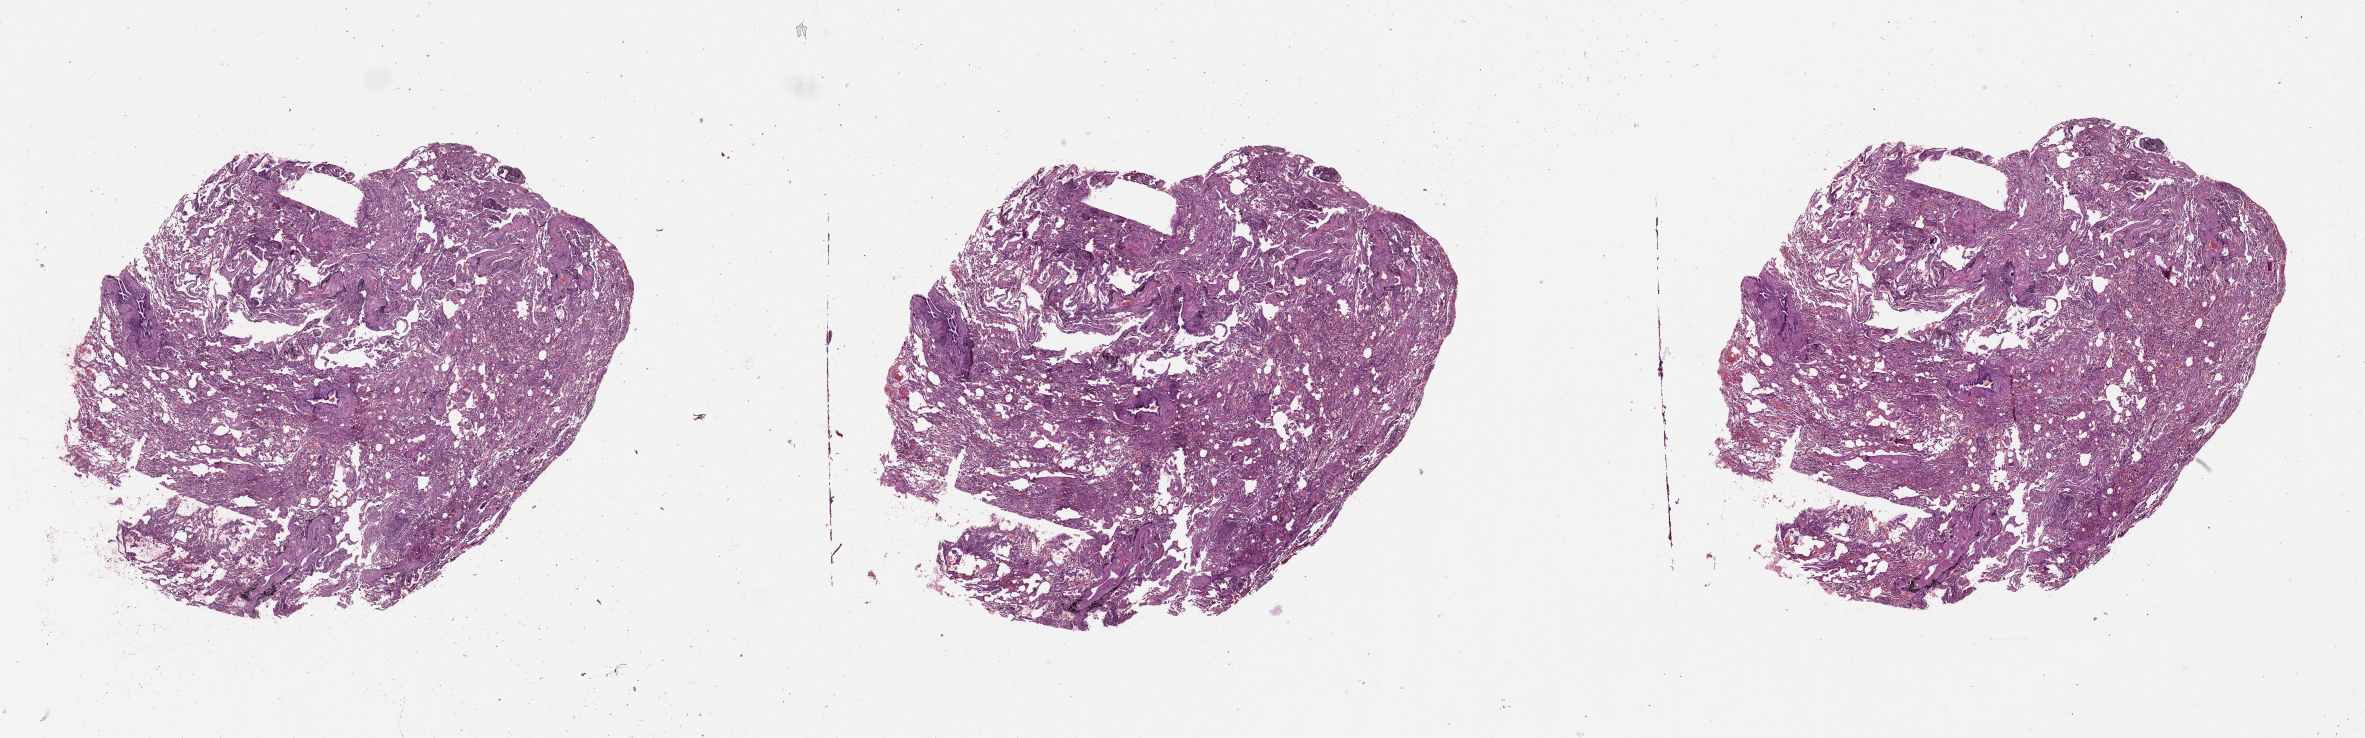
Digitized H&E-stained tissue section (whole slide), a low-resolution overview of the entire scanned area, about 38.1 x 11.9 mm (acquisition: 20x scan). Normal (non-tumour) tissue sample, lung. Patient: male, age 66 years.
This section: normal (non-tumour) tissue from the same patient. Patient diagnosis (cohort enrolment): squamous cell carcinoma (lung).